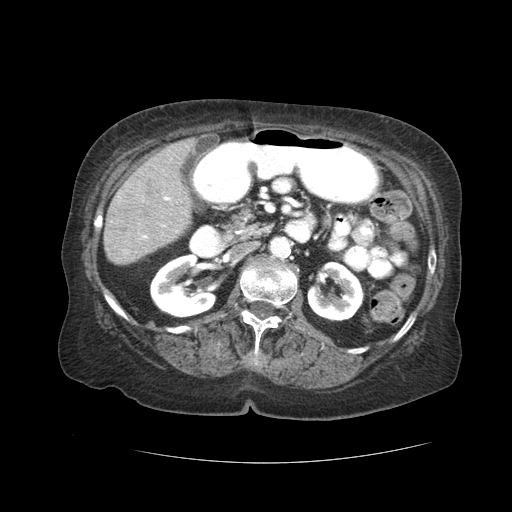
Contrast-enhanced abdominal CT (liver protocol), one axial slice; position 7 of 59 along the scan axis; 120 kVp; soft-tissue window (W 400 / L 40 HU); 2.5 mm slice thickness; 512 × 512 image matrix, field of view 380 × 380 mm. From the clinical record (not read from this slice): diagnosis: hepatocellular carcinoma (patient treated with transarterial chemoembolisation; whether this scan precedes or follows treatment is not stated here); TNM stage (as recorded): Stage-I; Child-Pugh class: A; tumour nodularity: uninodular.
Outlined on this slice (semi-automatic segmentation, software-assisted and operator-edited):
- liver parenchyma outside the tumour (the mass and vessels are separate outlines, so this box may not span the whole liver): bounding box <104,138,197,264> (left, top, right, bottom; pixels)
- liver vessels: <142,197,171,238>